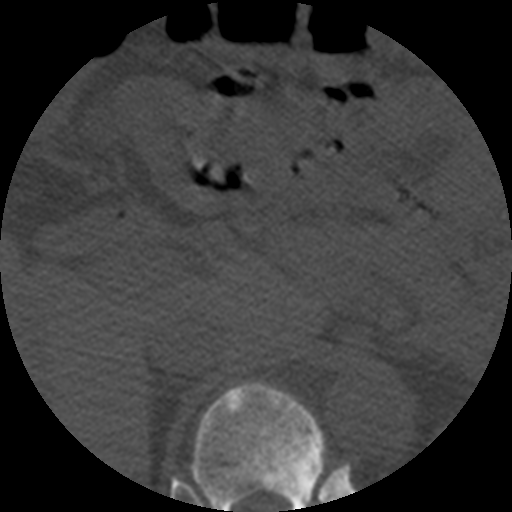
CT including the spine, one axial slice. Slice 248 of 508 in the series (ordered by position). Reconstruction kernel STANDARD. 120 kVp. Bone window (W 1800 / L 400 HU). 1.25 mm slice thickness. 512 × 512 image matrix. Patient age 57 years. From the clinical record (not read from this slice): primary cancer: prostate.
Outlined on this slice (semi-automatic segmentation, software-assisted and operator-edited):
- T11 vertebra: bounding box [x1, y1, x2, y2] px = [191, 382, 327, 512]